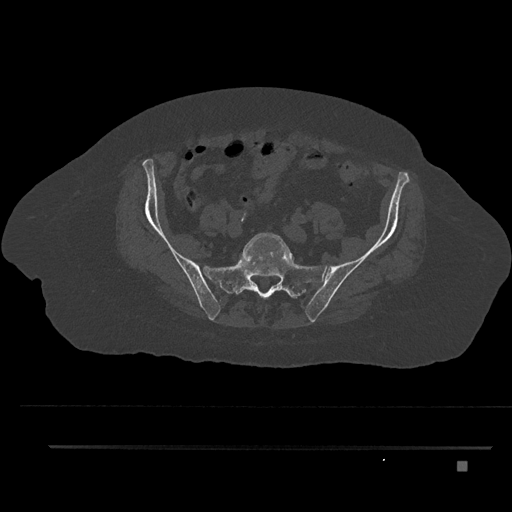
CT including the spine, one axial slice. Position 10 of 797 along the scan axis. 120 kVp. Bone window (W 1800 / L 400 HU). 512 × 512 image matrix, field of view 437 × 437 mm. Female patient, age 76 years. Case-level facts recorded for this patient, not image findings: primary cancer: lung; vertebrae with lytic lesions (as recorded): T11, L3.
Outlined on this slice (semi-automatically segmented with operator editing):
- L5 vertebra: bounding box (x1, y1, x2, y2) in pixels: (243, 232, 292, 294)